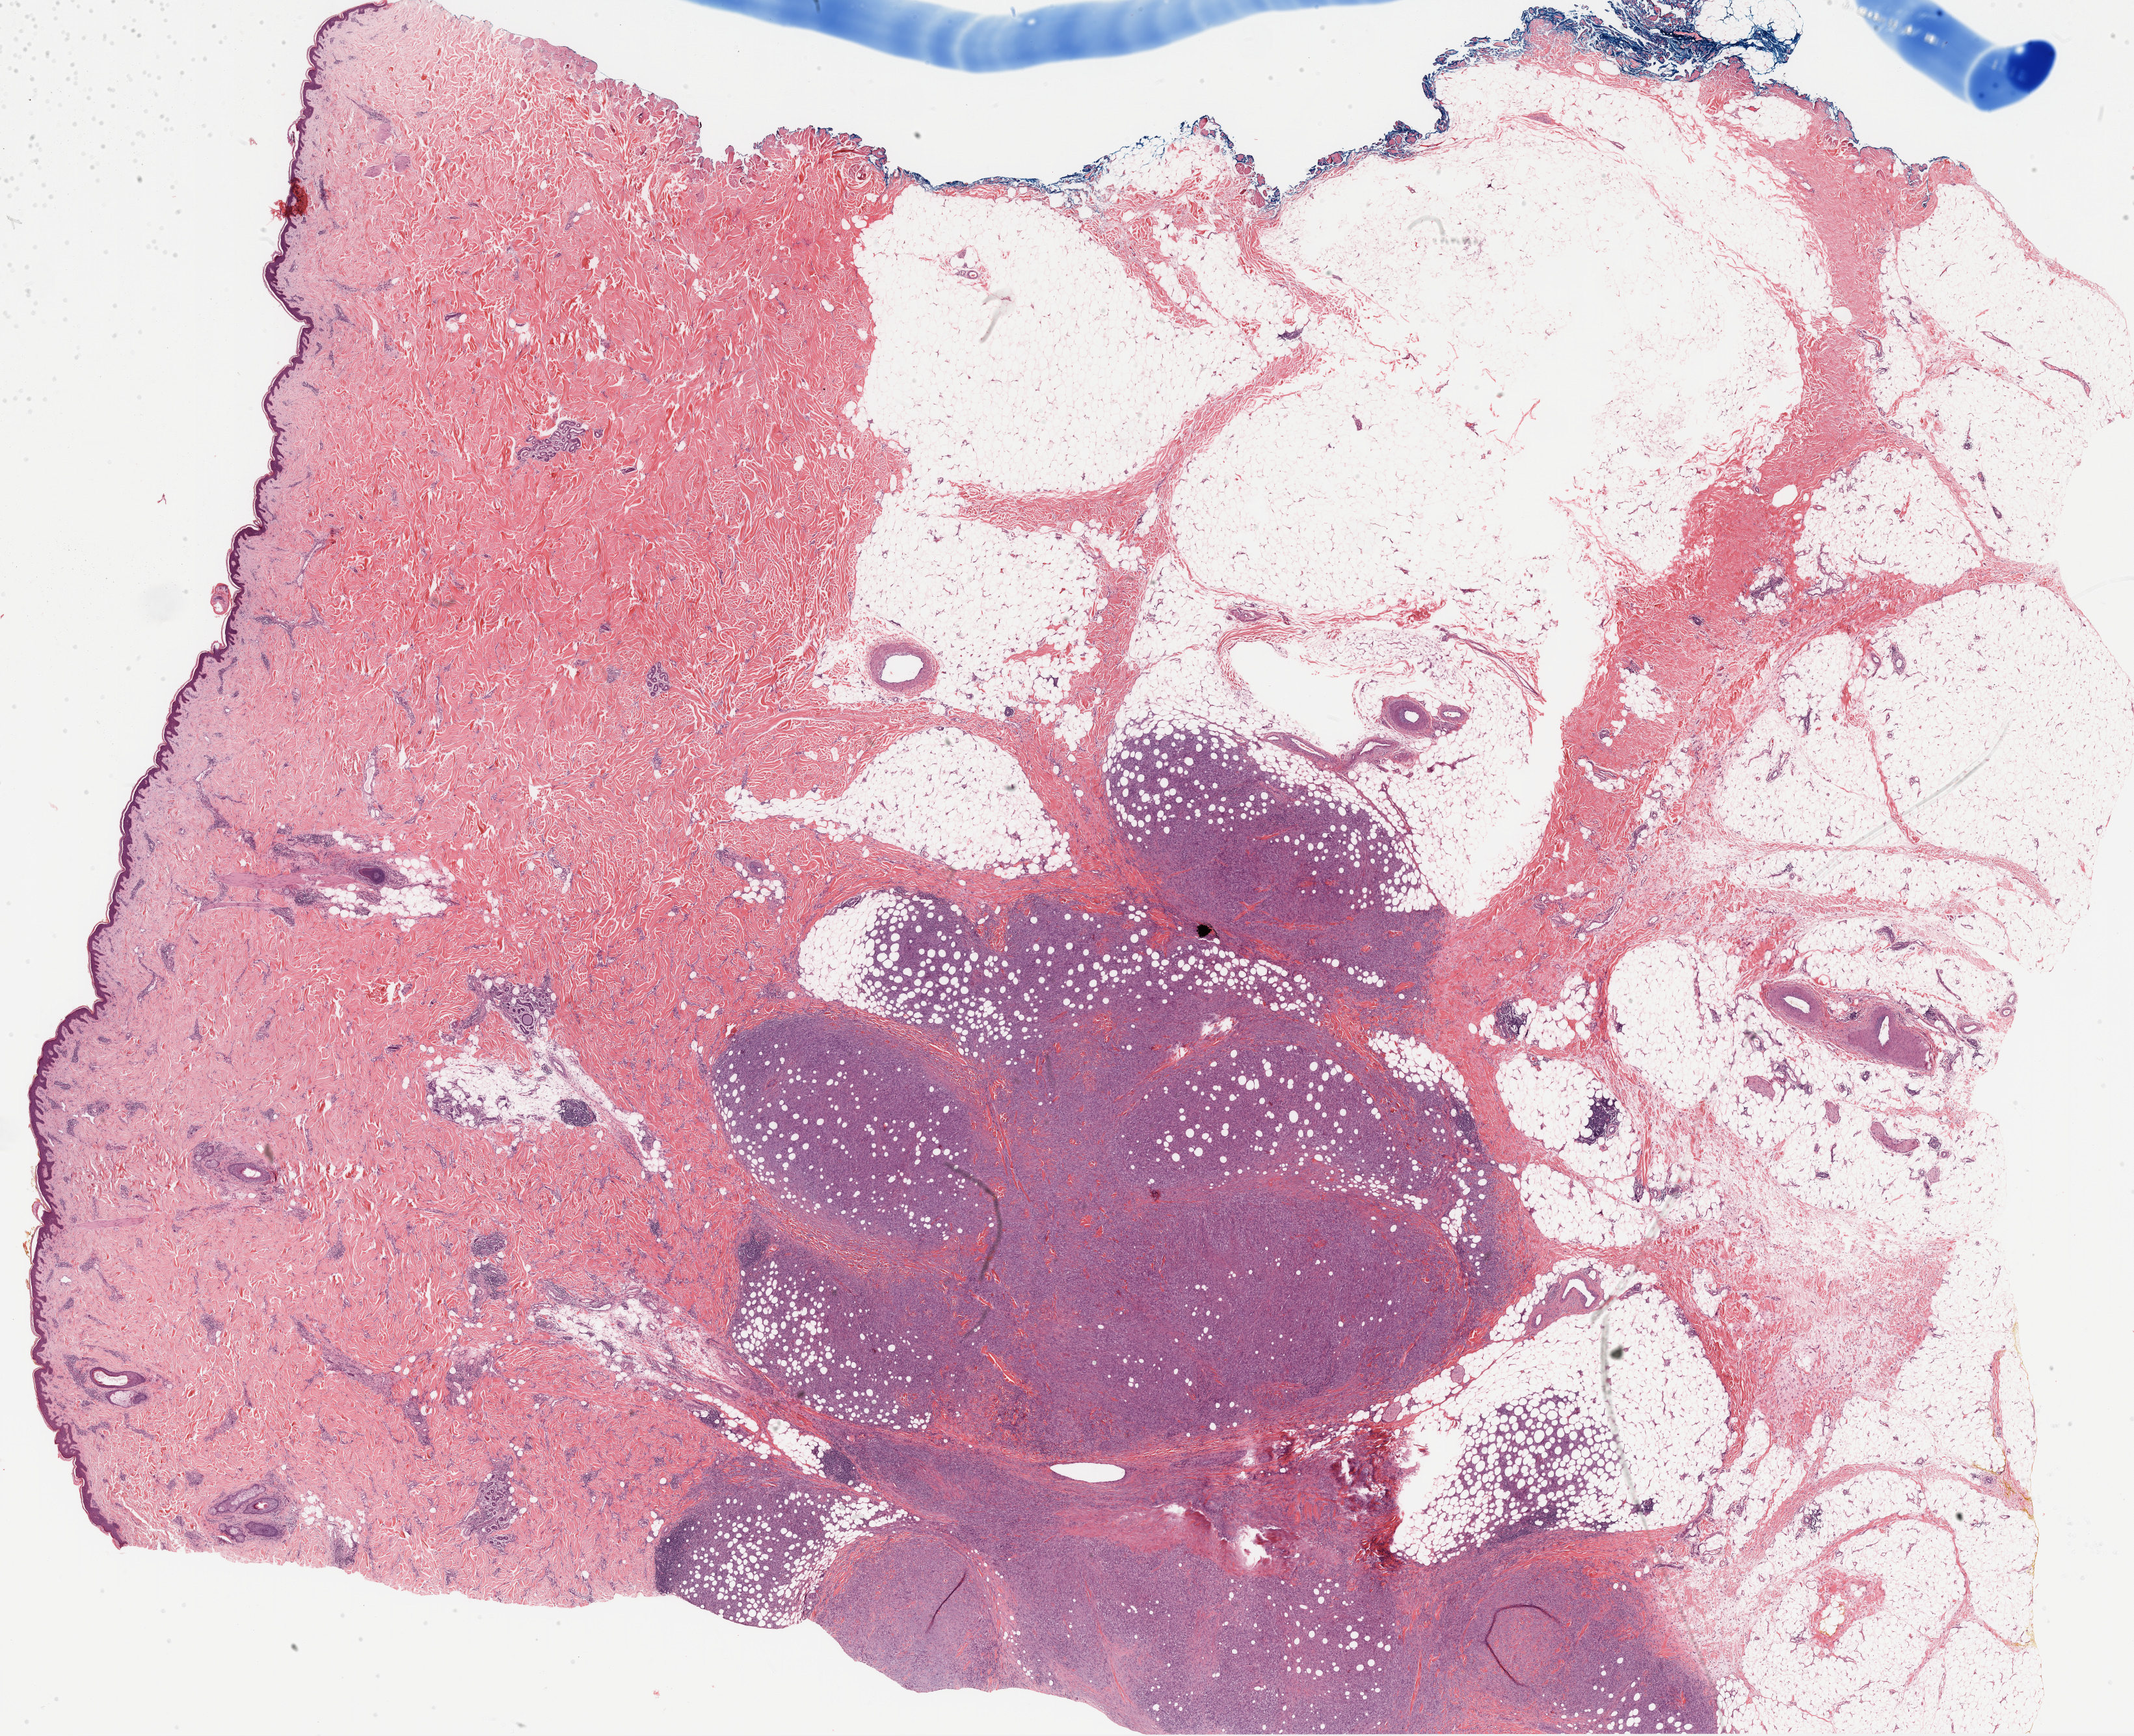
H&E whole-slide image, shown as a low-resolution overview of the whole scanned area (about 26.5 x 21.5 mm); FFPE section; metastatic tumour sample, sampled site not recorded. Patient: male, age at initial diagnosis 68 years.
This section: metastatic tumour tissue. Patient diagnosis: Malignant melanoma, NOS.